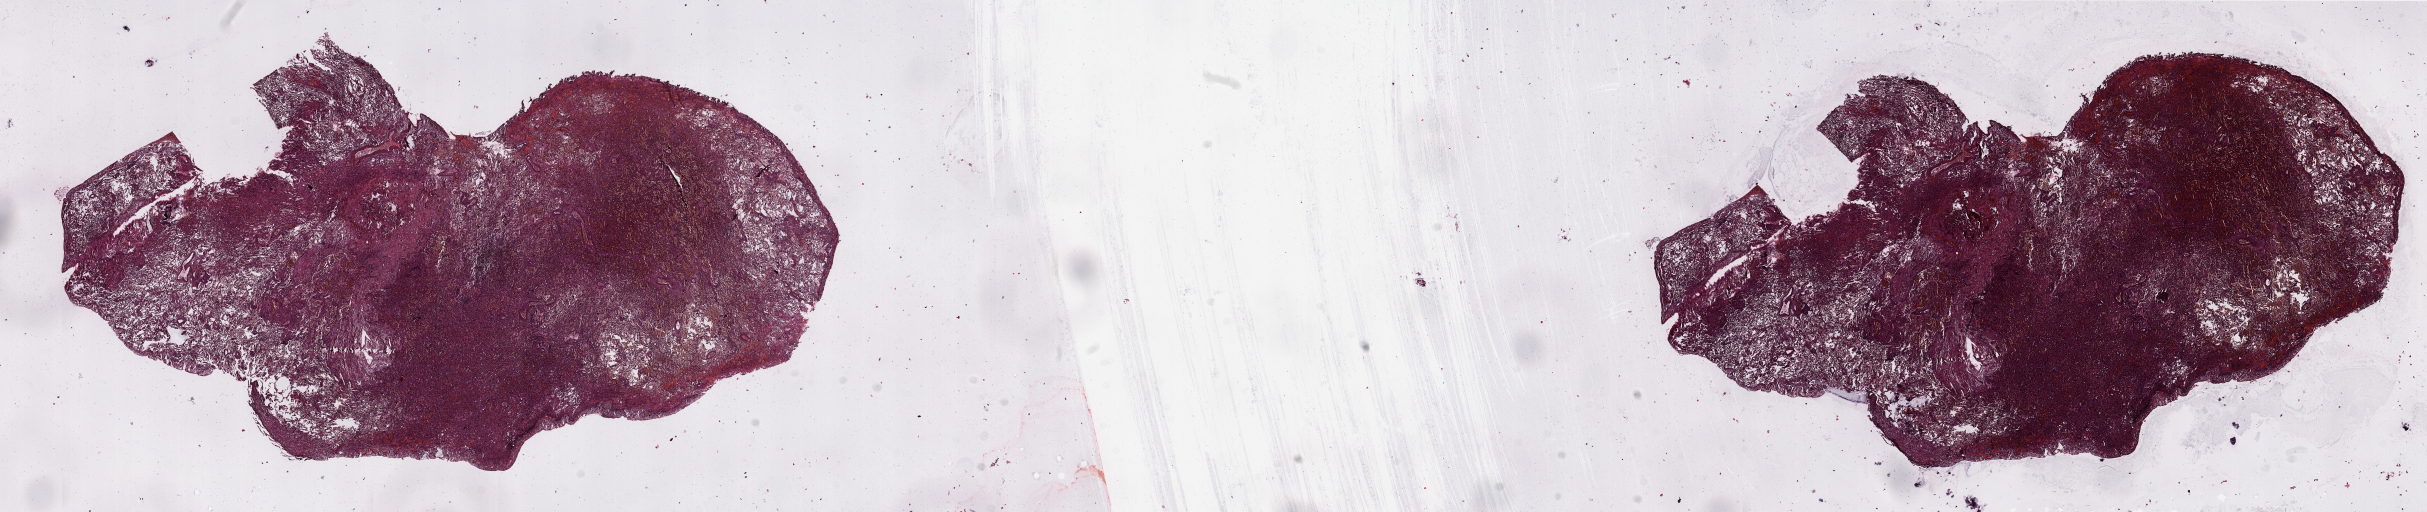
Digitized H&E tissue section (whole slide) — whole scanned area (about 38.4 x 8.1 mm, slide scanned at 20x) shown as a low-resolution overview. Normal (non-tumour) tissue sample, lung. Patient: male, age 66 years.
This section: normal (non-tumour) tissue from the same patient. Patient diagnosis: Squamous cell carcinoma, NOS.